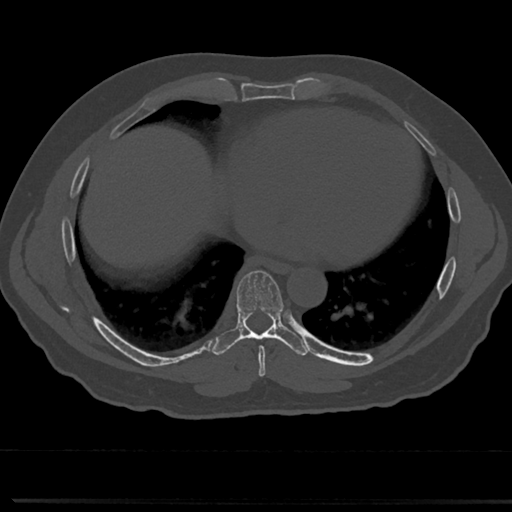
CT including the spine, one axial slice. Position 365 of 817 along the scan axis. 120 kVp. Bone window (W 1800 / L 400 HU). 512 × 512 image matrix, field of view 355 × 355 mm. Male patient, age 61 years. Case-level facts recorded for this patient, not image findings: primary cancer: prostate.
Structures marked on this image (semi-automatically segmented with operator editing):
- T7 vertebra: bounding box (x1, y1, x2, y2) in pixels: (236, 272, 287, 359)
- T8 vertebra: (237, 322, 283, 335)